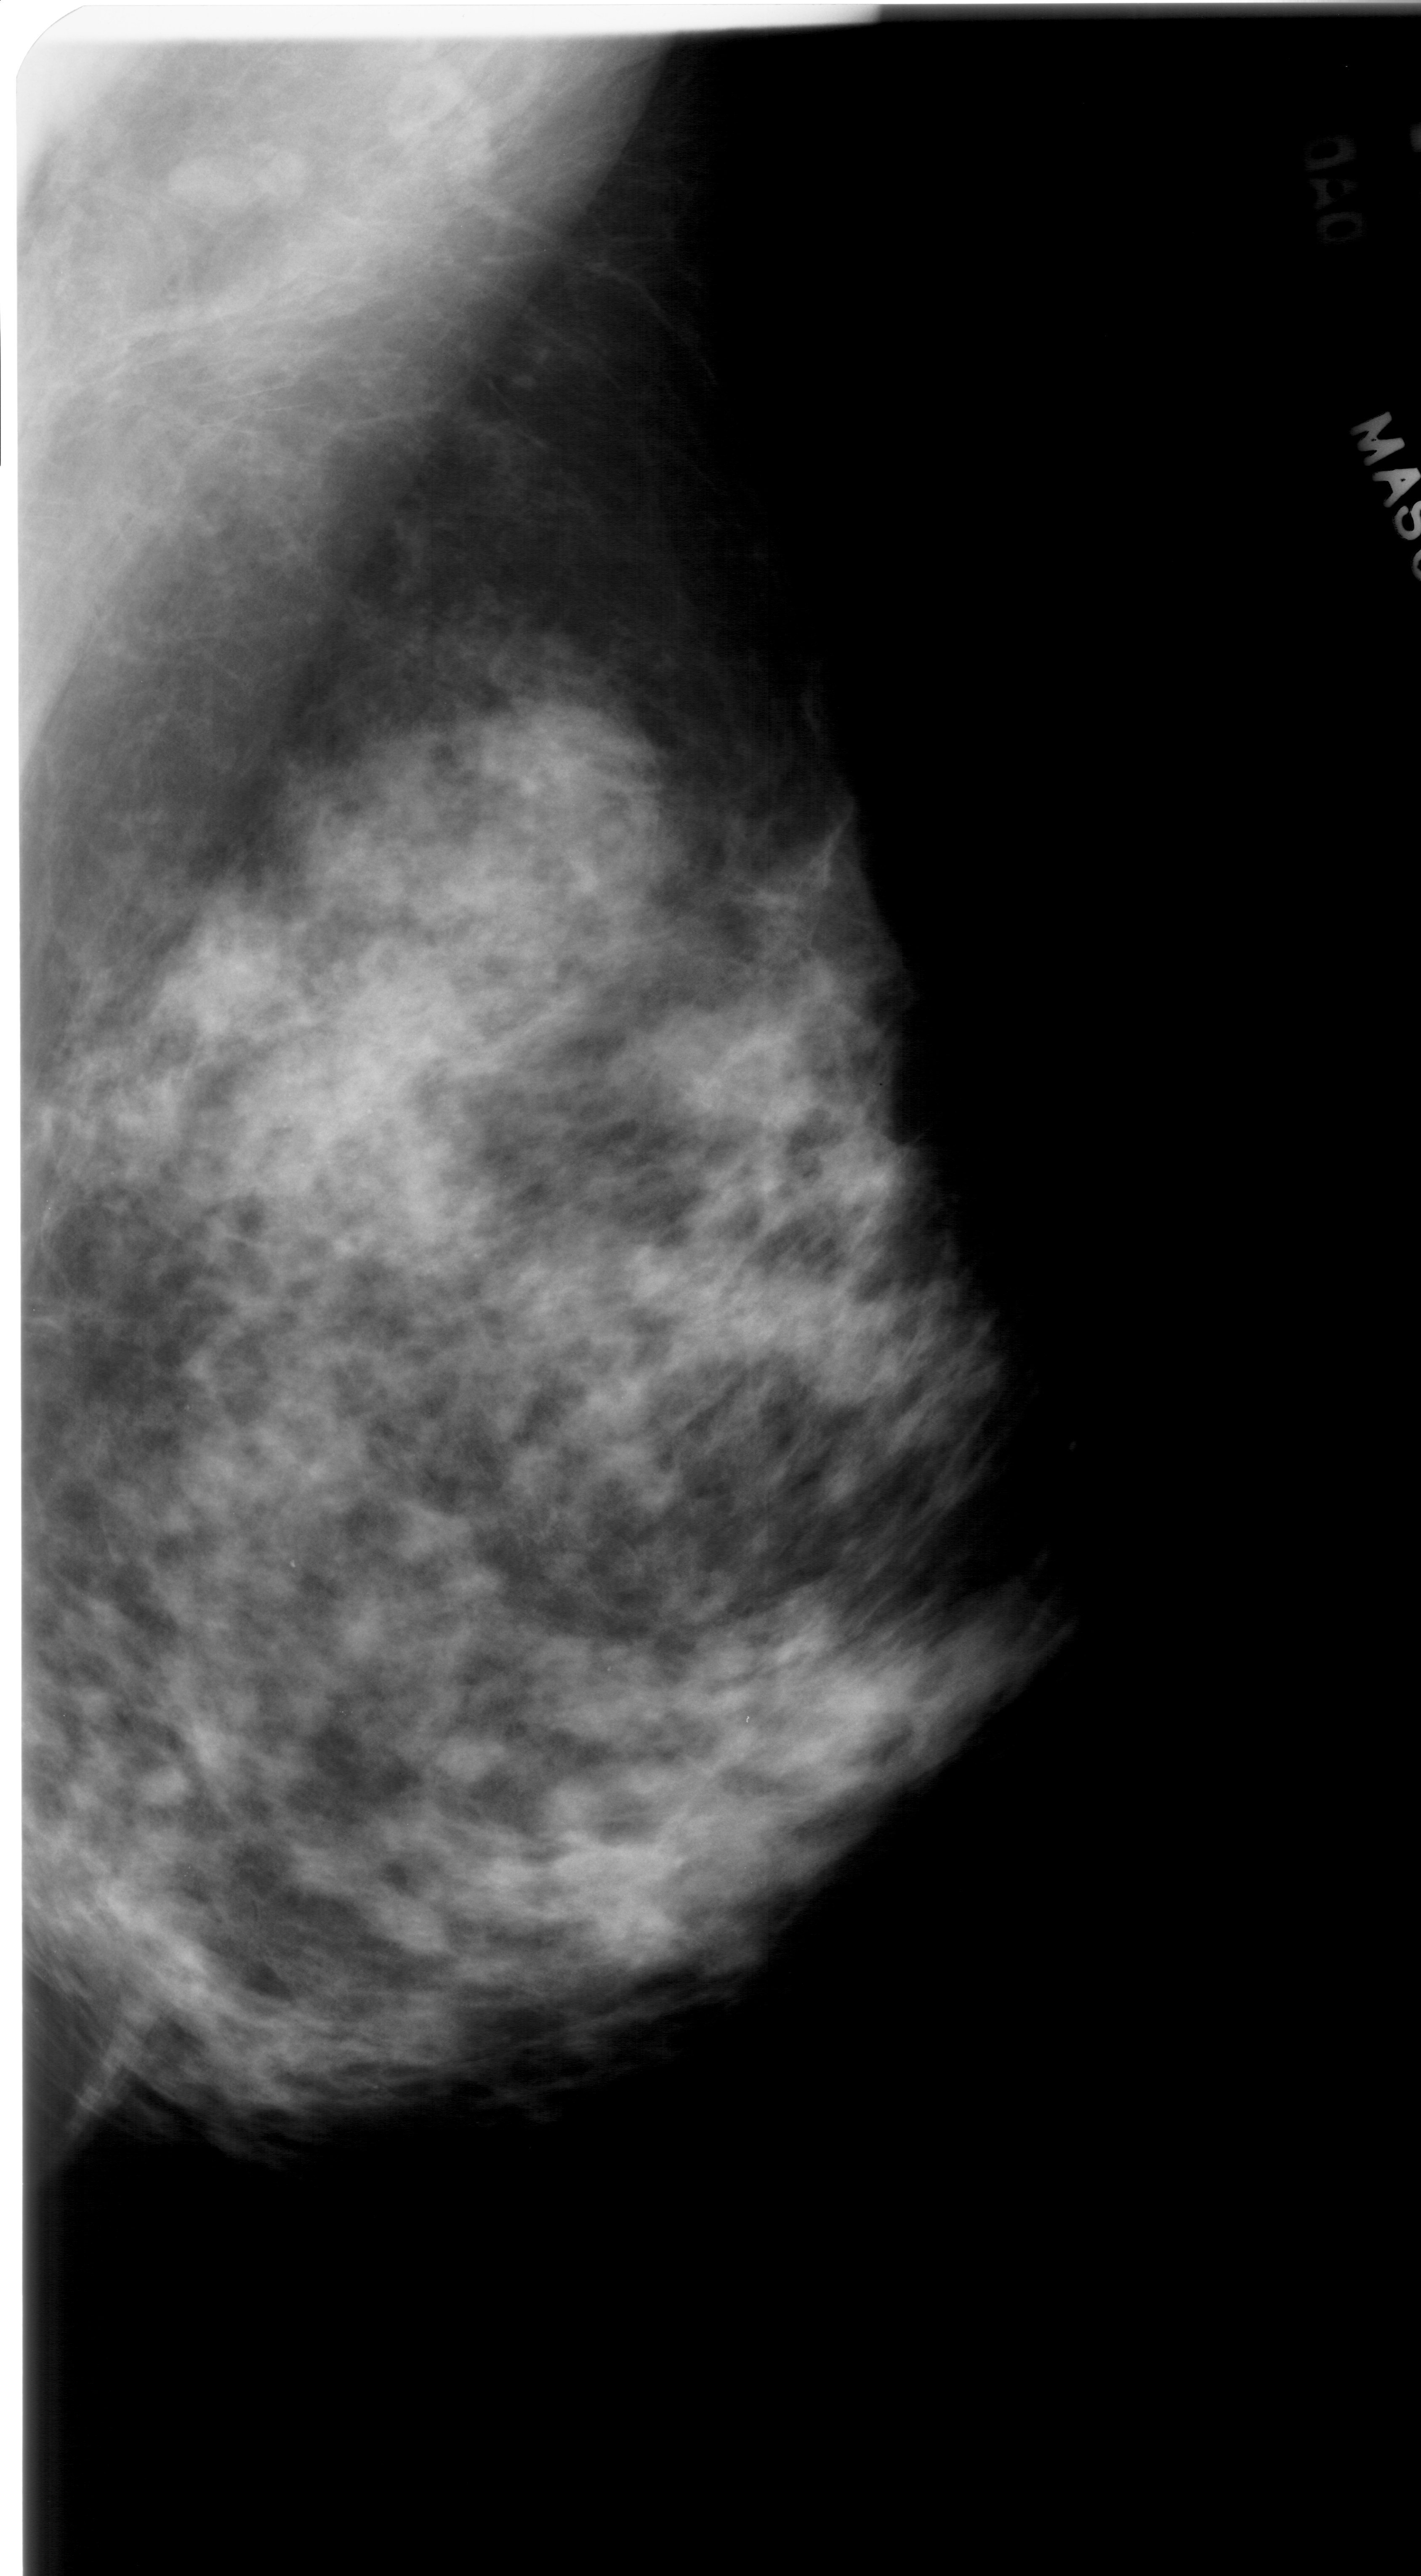
Scanned film-screen mammogram, right breast, mediolateral oblique (MLO) view, BI-RADS breast density category 3 (scale 1–4).
Marked abnormality: calcifications, morphology pleomorphic, distribution clustered; BI-RADS assessment category 4; pathology (as recorded): benign.